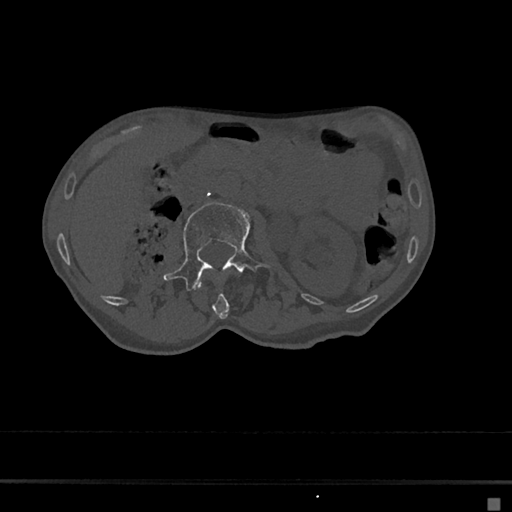
CT including the spine, one axial slice. Reconstruction kernel Br40s/3. Bone window (W 1800 / L 400 HU). 0.5 mm slice thickness. 512 × 512 image matrix, field of view 360 × 360 mm. Female patient, age 68 years. Case-level facts recorded for this patient, not image findings: primary cancer: renal.
Outlined on this slice (semi-automatically segmented with operator editing):
- L1 vertebra: box from (x=197, y=274) to (x=238, y=319) px
- L2 vertebra: (x=163, y=202)–(x=271, y=292)